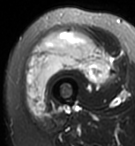
MRI of an extremity soft-tissue mass, one axial slice; slice 32 of 95 in the series (ordered by position); T2-weighted fat-saturated; MR volume resampled by the dataset authors to the PET/CT grid (not the native acquisition matrix); 135 × 146 image matrix, field of view 132 × 143 mm. Female patient. From the clinical record (not read from this slice): histological type: pleiomorphic undifferentiated sarcoma; grade: high; site of the primary tumour: right quadricep.
Annotated regions visible in this slice (expert contour drawn on MRI and transferred to this co-registered scan by the dataset authors):
- gross tumour volume including surrounding oedema: bounding box [x1, y1, x2, y2] px = [25, 31, 109, 117]
- gross tumour volume (mass): [25, 31, 109, 117]